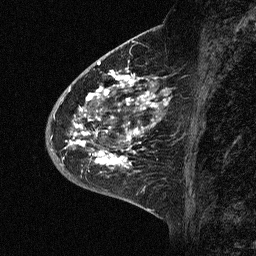
Breast MRI (dynamic contrast-enhanced), one sagittal slice; position 23 of 64 along the scan axis; dynamic contrast-enhanced study with each time point stored as its own series, time point 2 of 3 at this slice position (early post-contrast, ordered by acquisition time); 1.5 T; TE 4.5 ms, TR 11 ms; 2.06 mm slice thickness; 256 × 256 image matrix. Female patient, age 46 years. From the clinical record (not read from this slice): setting: breast cancer imaged before/during neoadjuvant chemotherapy; receptor status: HER2-positive.
Annotated regions visible in this slice (semi-automatically segmented with operator editing):
- analysis volume of interest (the breast-tissue region the enhancement analysis was run in; not a lesion): bounding box (x1, y1, x2, y2) in pixels: (43, 72, 176, 177)
- tumour enhancement mask (voxels above the 90 % enhancement threshold inside the analysis volume of interest): (68, 72, 166, 172)